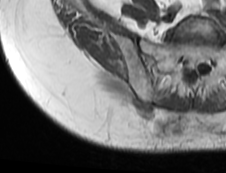
MRI of an extremity soft-tissue mass, one axial slice; slice 56 of 73 in the series (ordered by position); MR volume resampled by the dataset authors to the PET/CT grid (not the native acquisition matrix); 3.27 mm slice thickness; 226 × 173 image matrix, field of view 221 × 169 mm. Female patient. Case-level facts recorded for this patient, not image findings: histological type: spindle cell suggestive of myxofibrosarcoma; grade: intermediate; site of the primary tumour: right buttock.
Annotated regions visible in this slice (expert contour drawn on MRI and transferred to this co-registered scan by the dataset authors):
- gross tumour volume (mass): bounding box (x1, y1, x2, y2) in pixels: (118, 95, 185, 135)